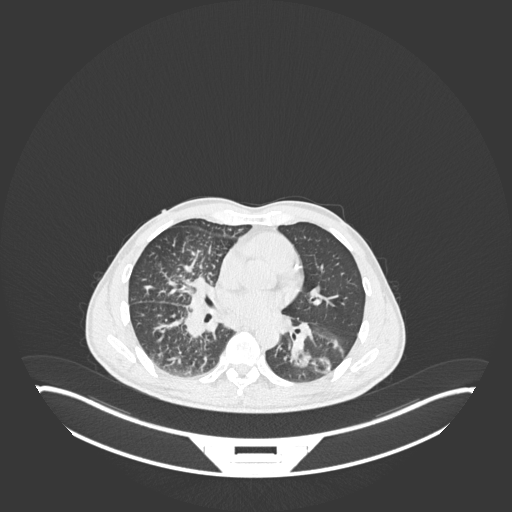
Chest CT, one axial slice; position 117 of 237 along the scan axis; reconstruction kernel B30f; 120 kVp; lung window (W 1500 / L -600 HU); 1 mm slice thickness; 512 × 512 image matrix, field of view 500 × 500 mm. Patient: male, 49 years. Case-level facts recorded for this patient, not image findings: clinical TNM (as recorded): T2b N1 M0.
Outlined on this slice (bounding box drawn by a radiologist):
- lung tumour (recorded histology: adenocarcinoma): bounding box (x1, y1, x2, y2) in pixels: (288, 320, 345, 378)